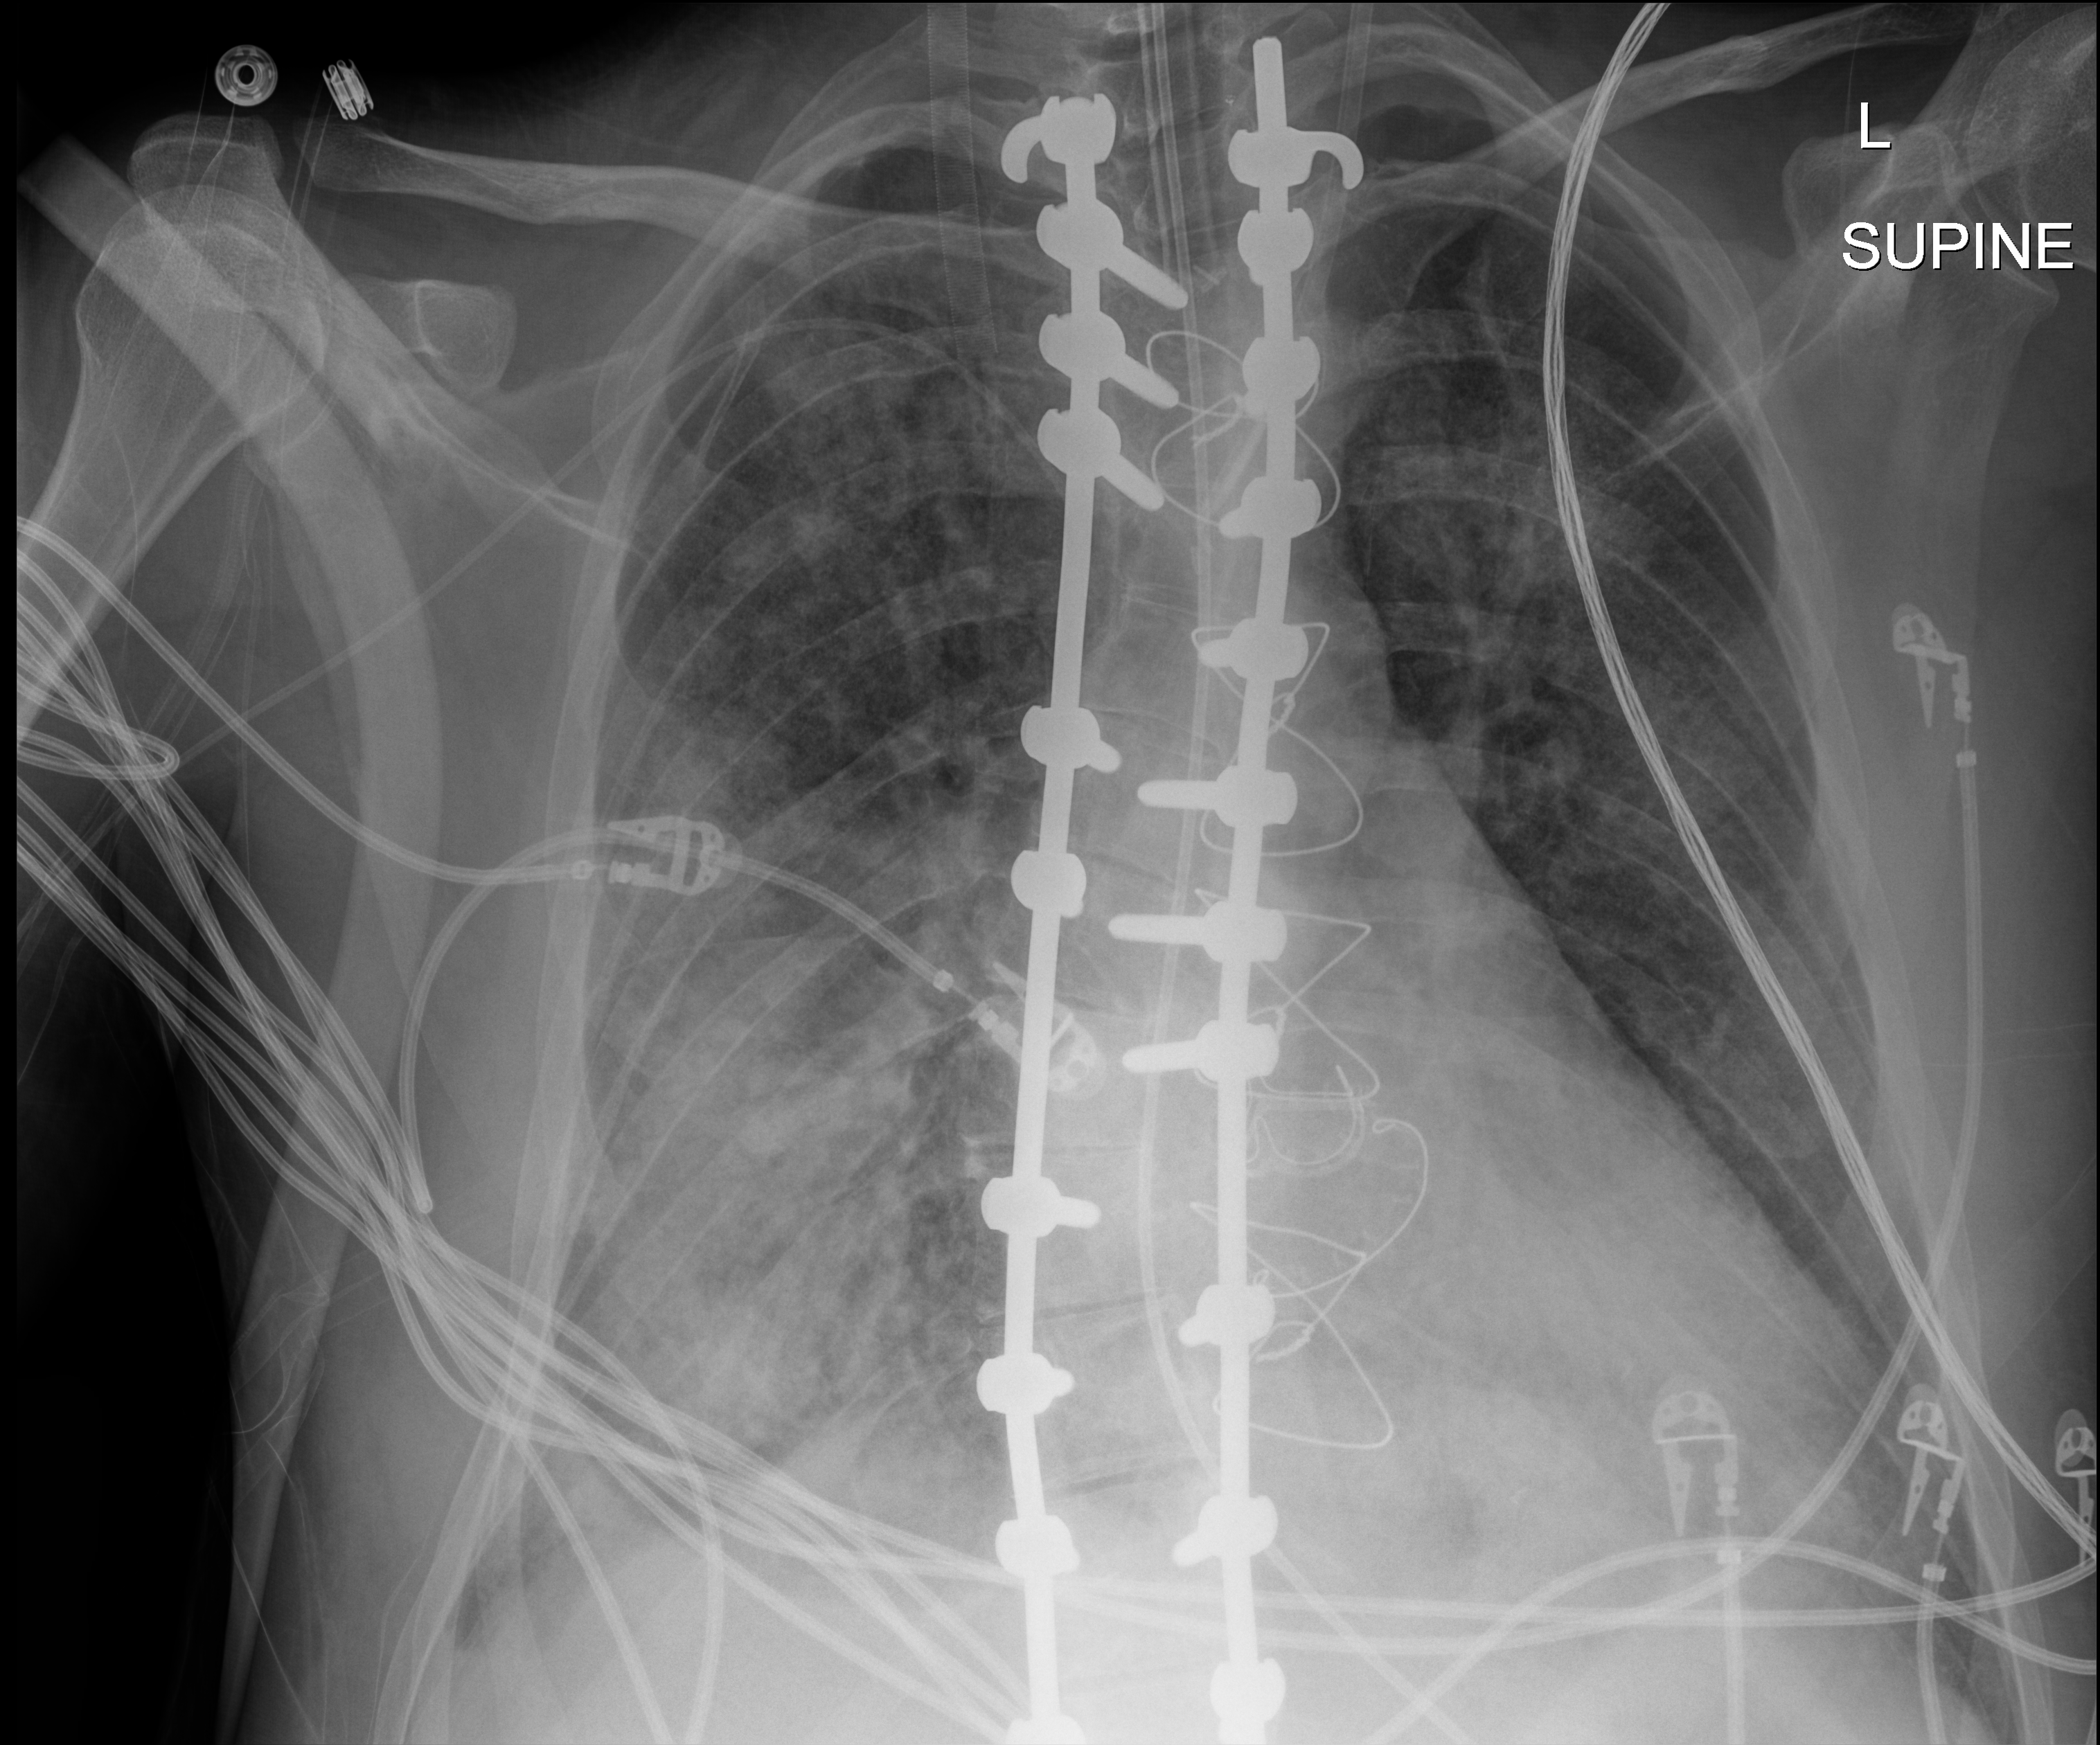
Chest X-ray (portable); anteroposterior (AP) projection. Adult patient hospitalised with COVID-19, age 18–59 years.
Hospital-stay facts (about this admission, not read from this image; timing relative to this image not recorded): mechanically ventilated during this hospital stay: yes; chronic kidney disease (admission record): no.